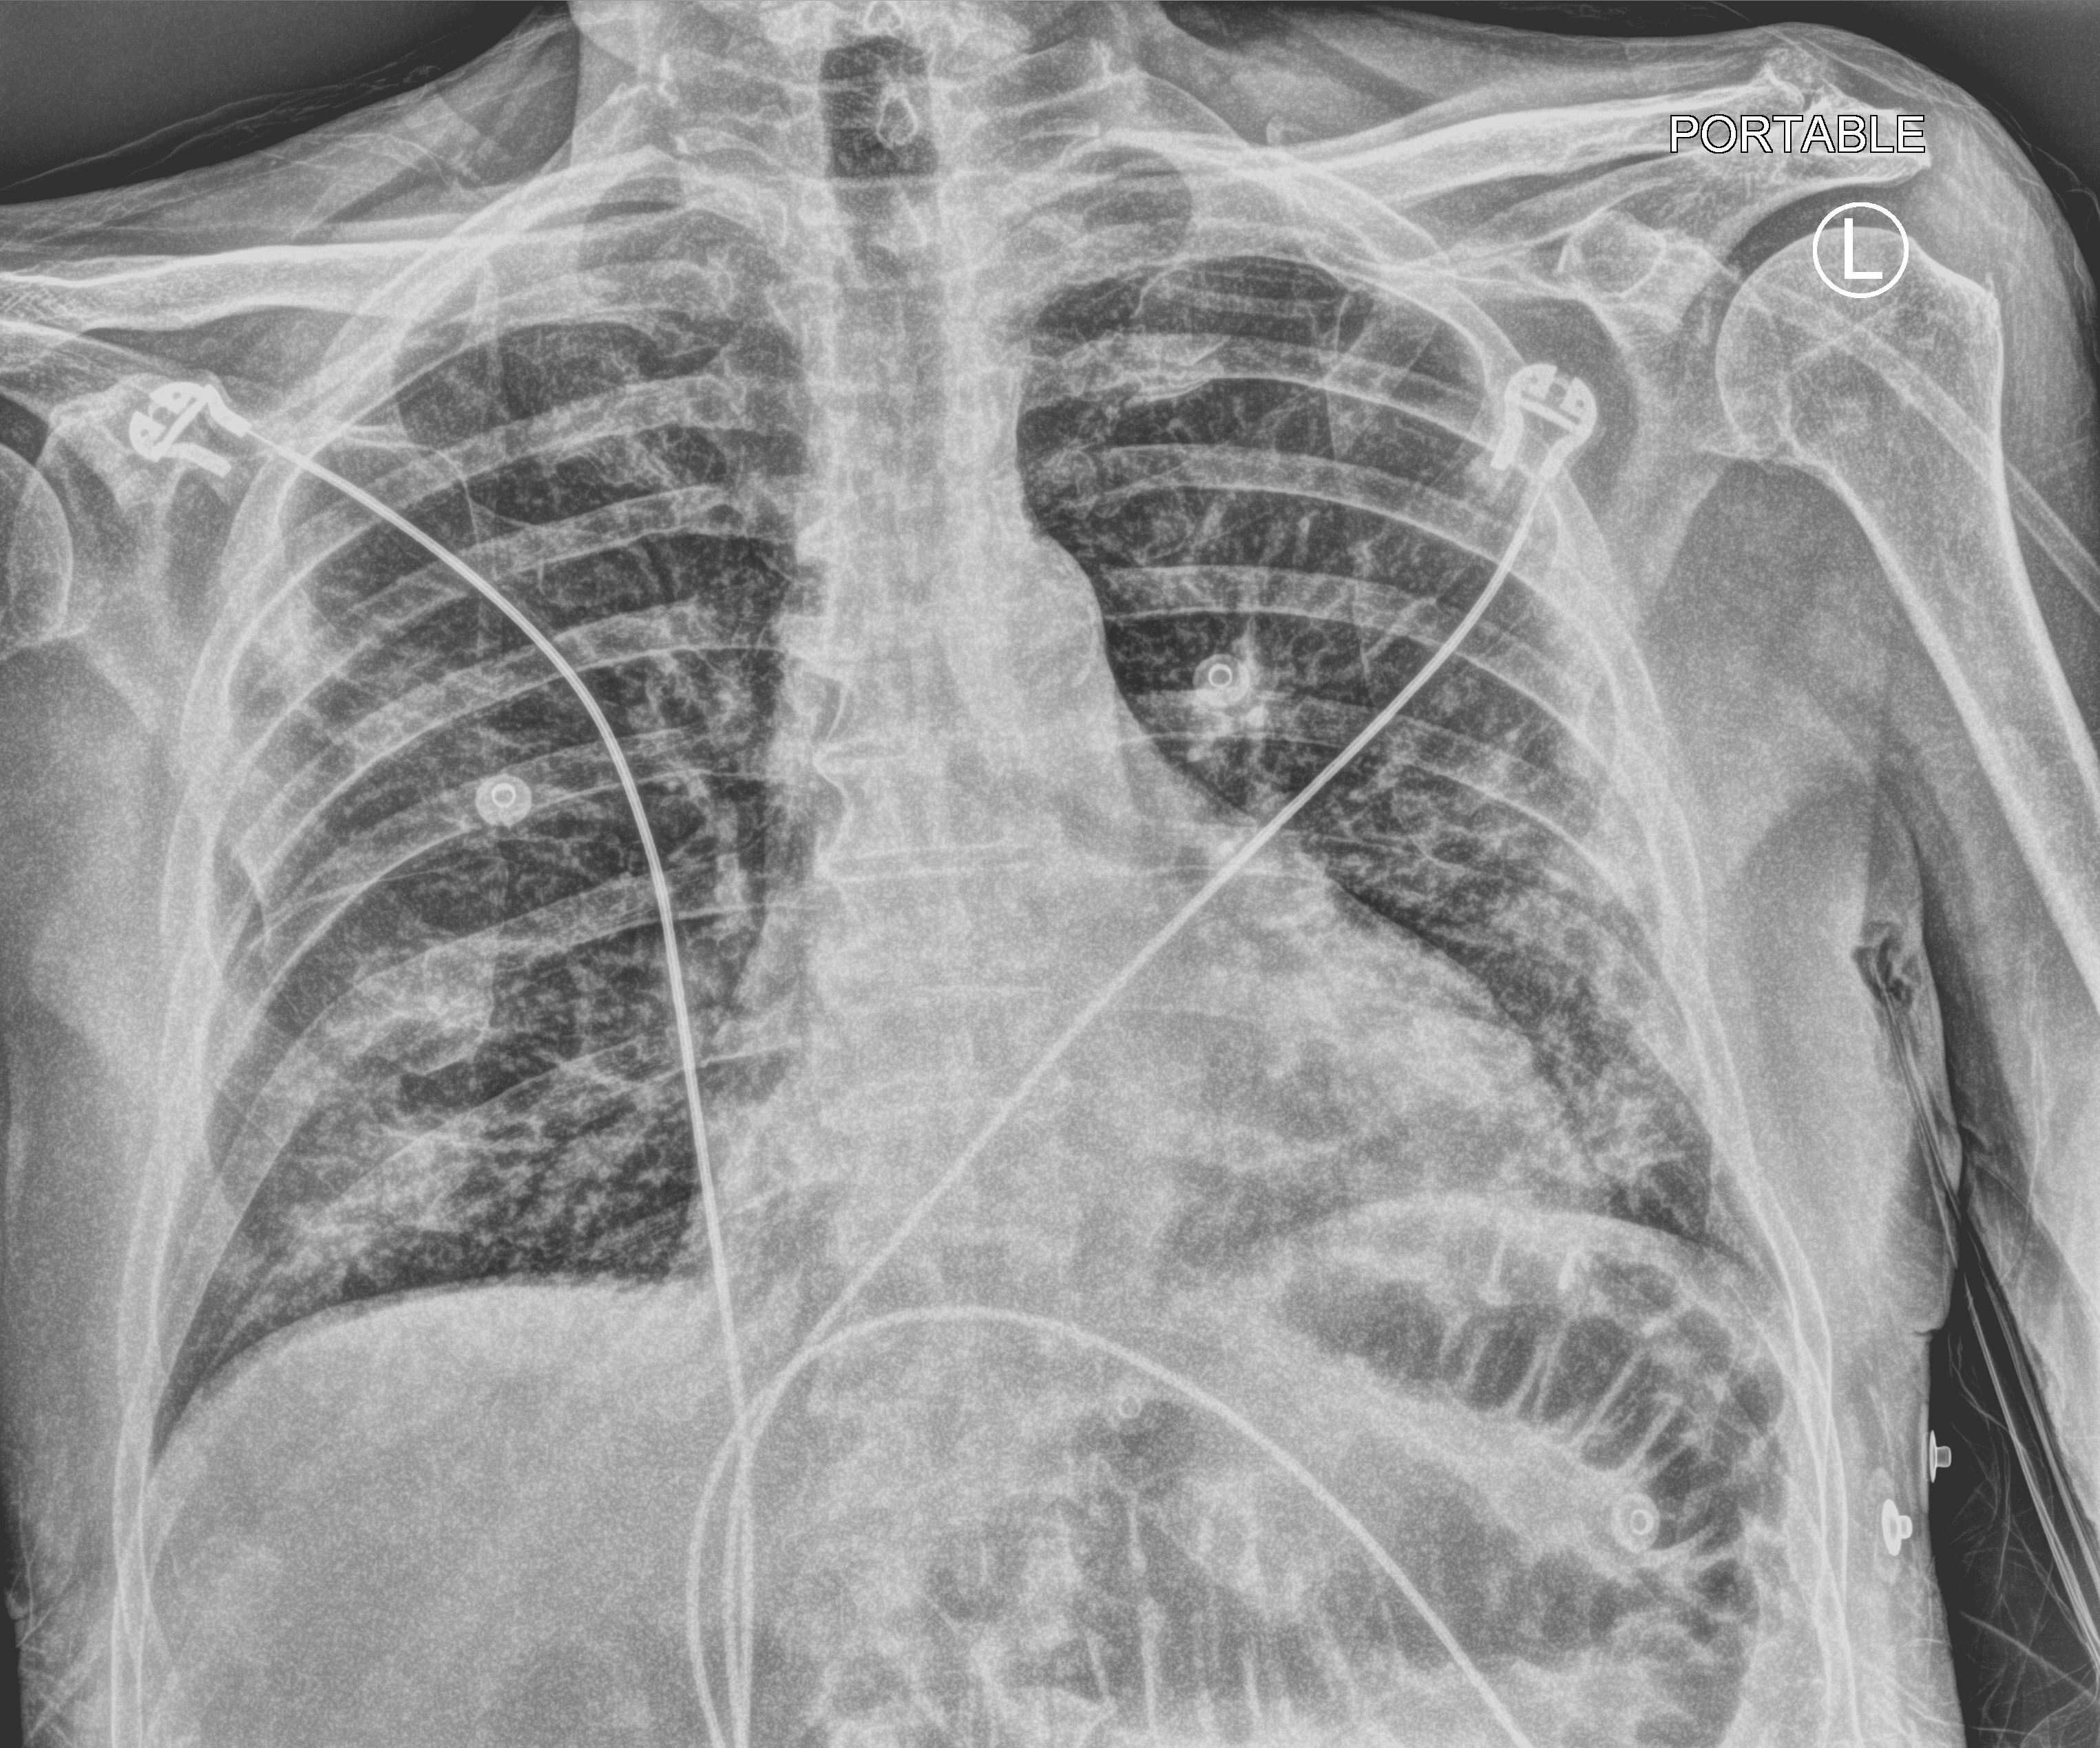
Portable chest radiograph, anteroposterior (AP) projection. Male patient hospitalised with COVID-19, age 75–90 years.
From the hospital-stay record, not from the radiograph (when in the stay this image was taken is not recorded): mechanically ventilated during this hospital stay: no.